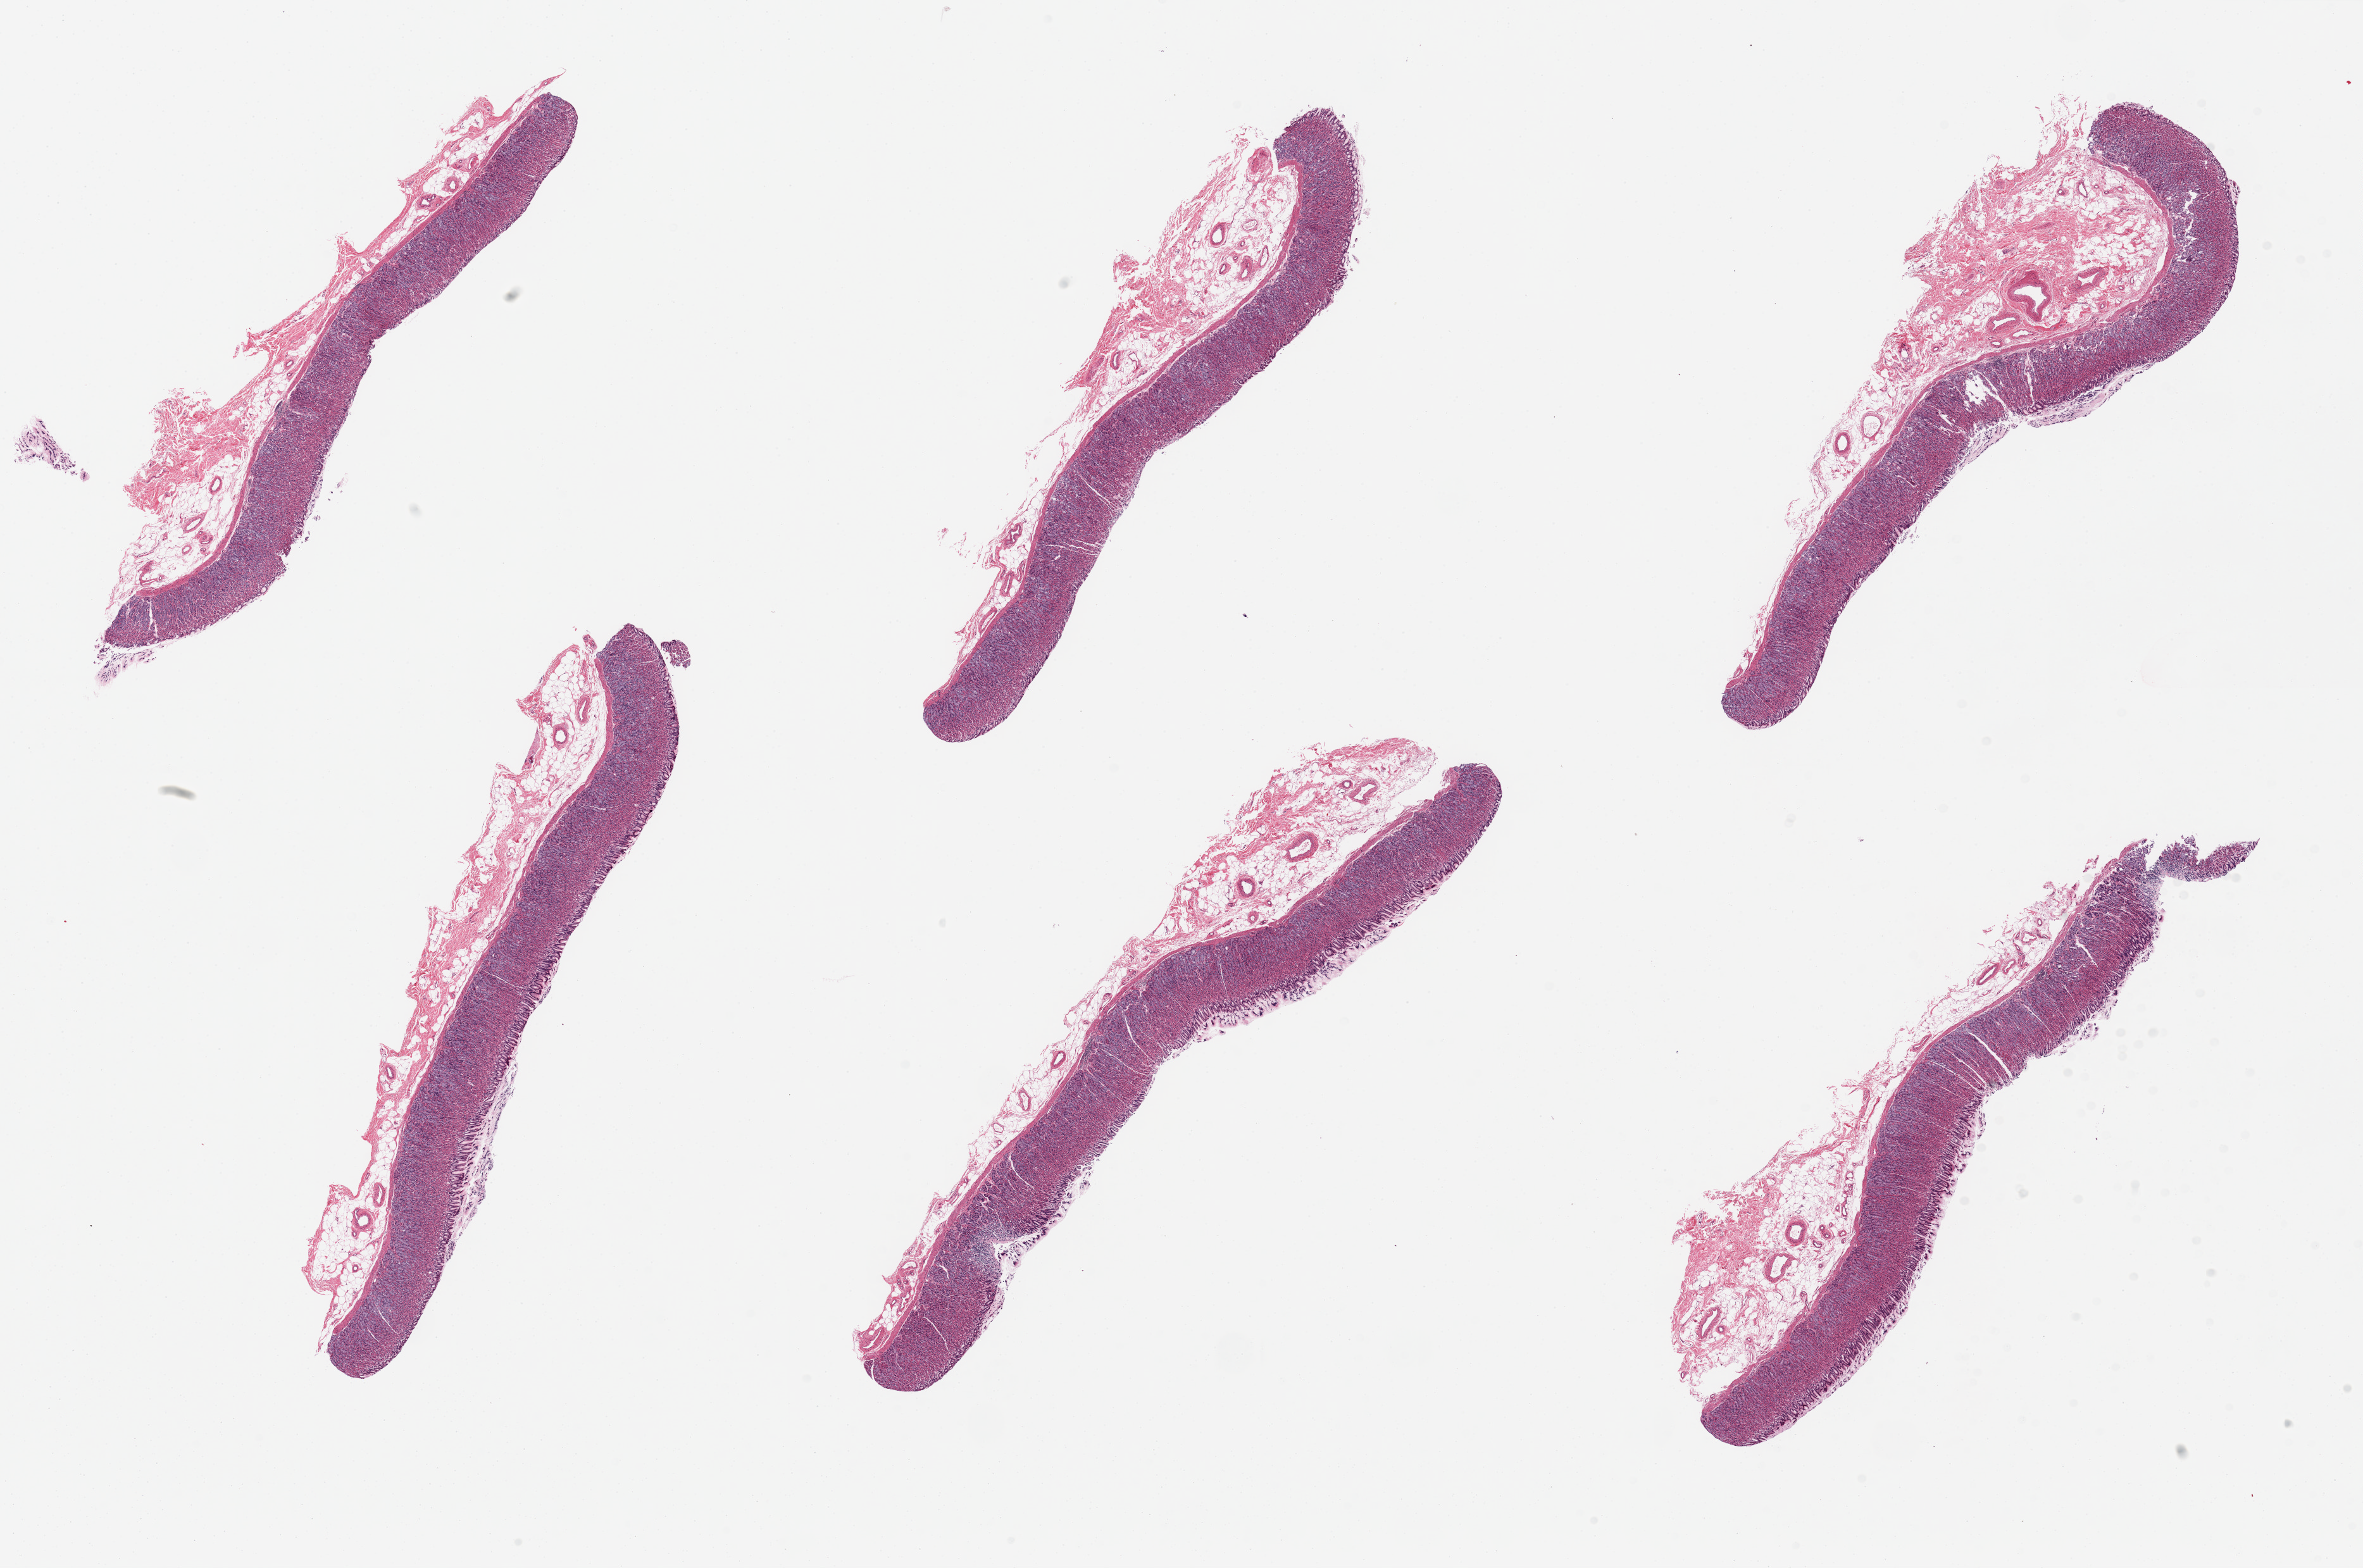
Whole-slide image, hematoxylin and eosin (H&E) stain, whole scanned area (about 29.5 x 19.6 mm, from a 20x scan) shown as a low-resolution overview. PAXgene-fixed paraffin-embedded (PFPE) section. Target tissue: stomach. Donor tissue sample. Female donor.
* reviewer comment on this tissue sample: 6 pieces, mucosa and submucosa